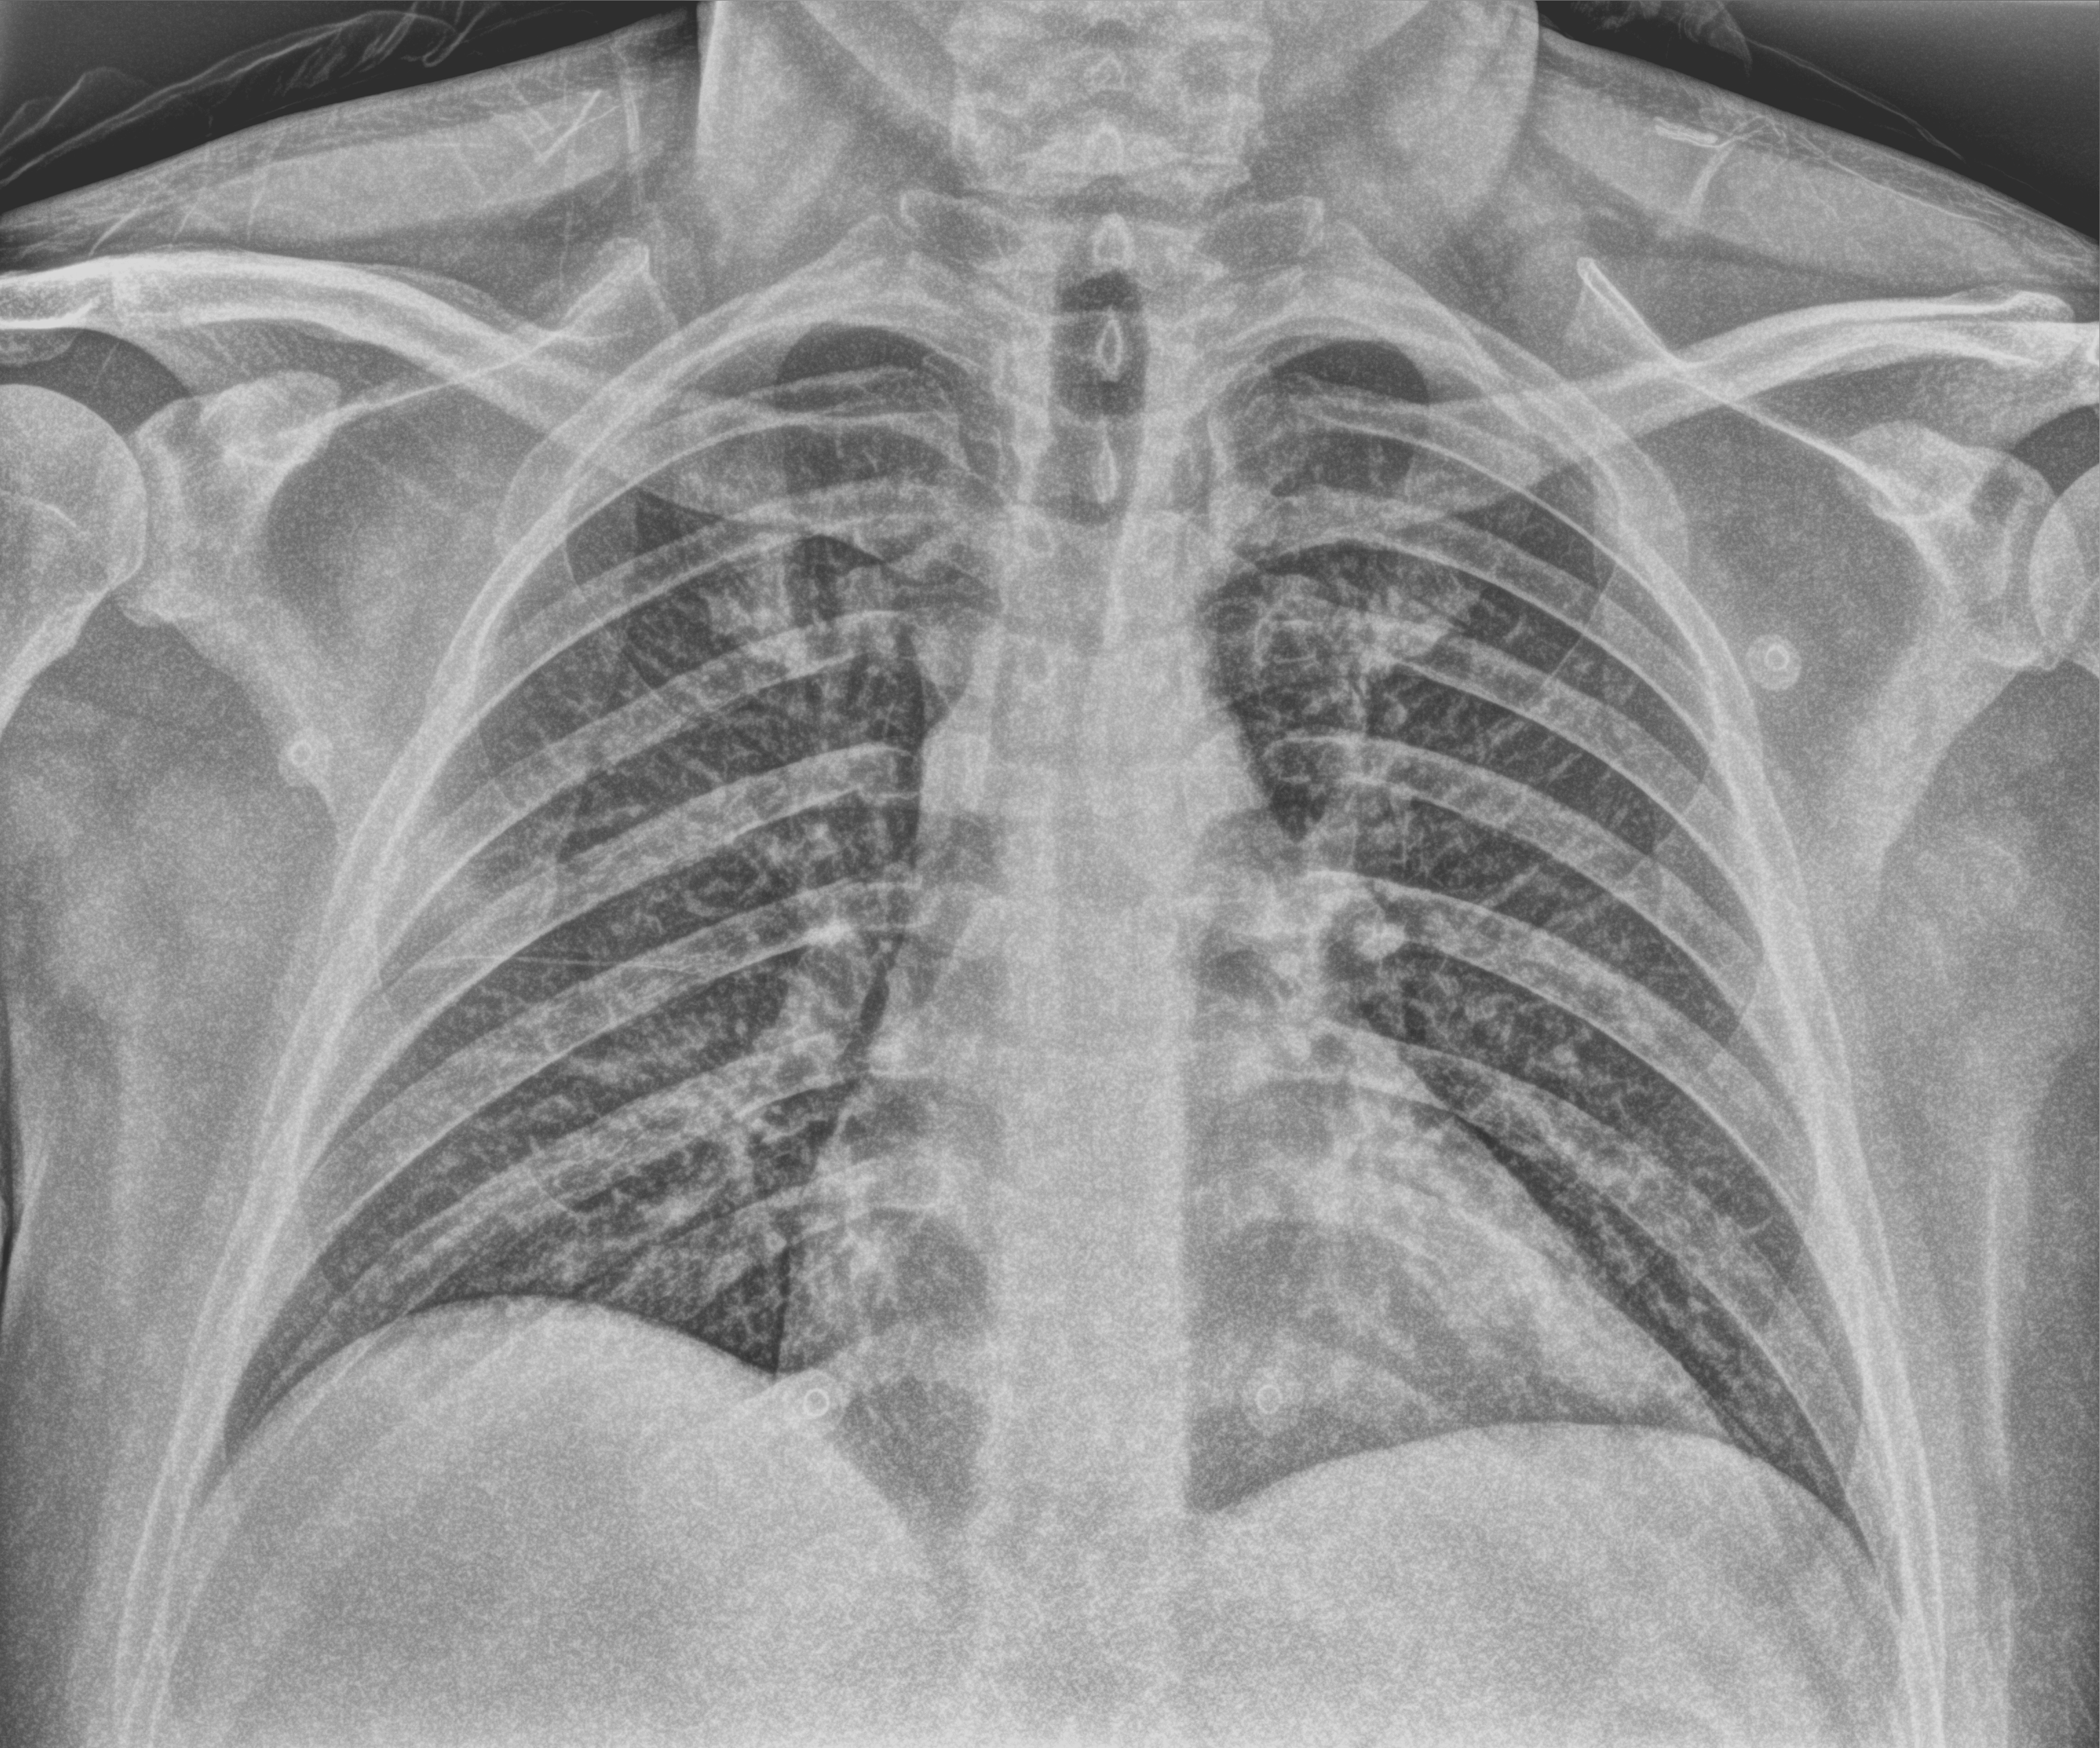
Chest X-ray (portable); anteroposterior (AP) projection. Male patient hospitalised with COVID-19, age 18–59 years.
Hospital-stay facts (about this admission, not read from this image; timing relative to this image not recorded): mechanically ventilated during this hospital stay: no; admitted to intensive care during this hospital stay: no.